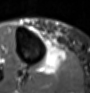
MRI of an extremity soft-tissue mass, one axial slice. Slice 33 of 60 in the series (ordered by position). STIR. MR volume resampled by the dataset authors to the PET/CT grid (not the native acquisition matrix). 3.27 mm slice thickness. 90 × 93 image matrix. Female patient. Case-level facts recorded for this patient, not image findings: histological type: undifferentiated – high grade; grade: high; site of the primary tumour: right thigh.
Annotated regions visible in this slice (expert contour drawn on MRI and transferred to this co-registered scan by the dataset authors):
- gross tumour volume (mass): bounding box (x1, y1, x2, y2) in pixels: (40, 42, 68, 75)